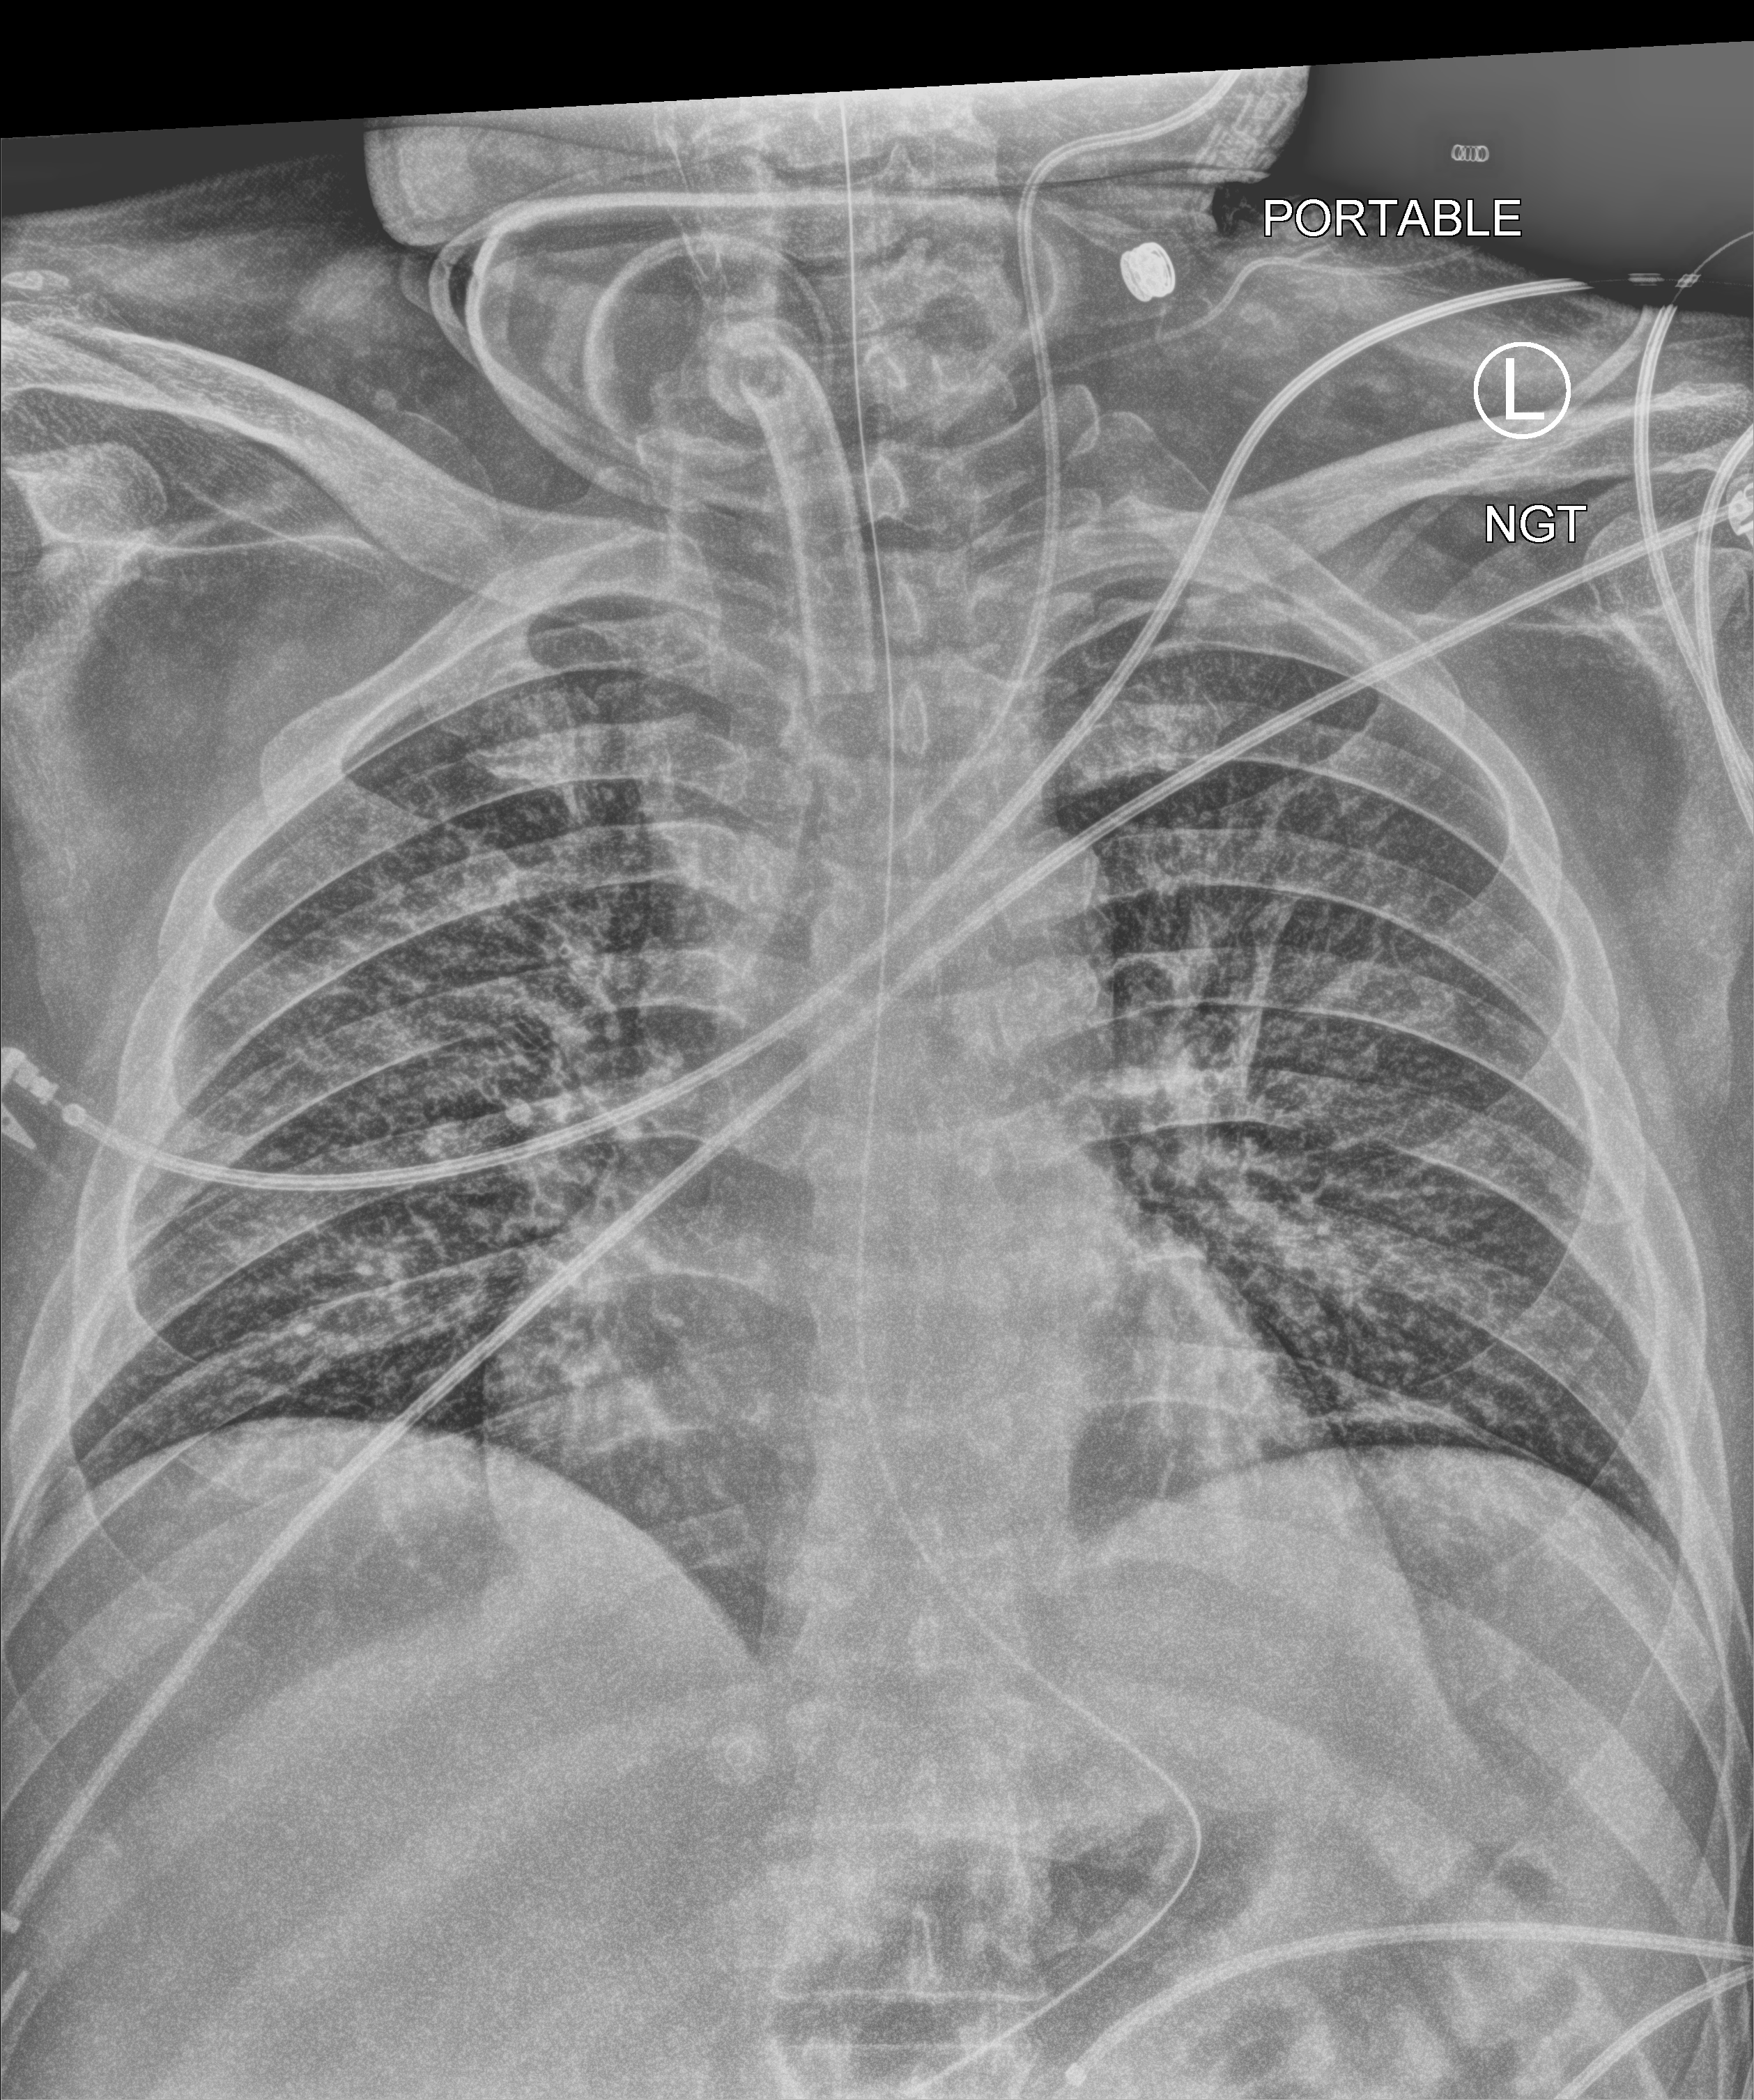
Chest X-ray (portable). Male patient hospitalised with COVID-19, age 18–59 years.
From the hospital-stay record, not from the radiograph (when in the stay this image was taken is not recorded): length of hospital stay: 65 days; admitted to intensive care during this hospital stay: yes.